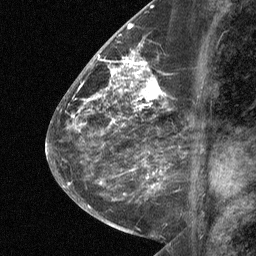
Breast MRI (dynamic contrast-enhanced), one sagittal slice. Position 28 of 64 along the scan axis. Dynamic contrast-enhanced study with each time point stored as its own series, time point 2 of 3 at this slice position (early post-contrast, ordered by acquisition time). 1.5 T. TE 4.8 ms, TR 27 ms. 2 mm slice thickness. 256 × 256 image matrix. Patient: female, 59 years. Case-level facts recorded for this patient, not image findings: setting: breast cancer imaged before/during neoadjuvant chemotherapy; receptor status: triple-negative.
Outlined on this slice (semi-automatic segmentation, software-assisted and operator-edited):
- analysis volume of interest (the breast-tissue region the enhancement analysis was run in; not a lesion): bounding box [x1, y1, x2, y2] px = [122, 58, 176, 109]
- tumour enhancement mask (voxels above the 90 % enhancement threshold inside the analysis volume of interest): [122, 58, 160, 102]